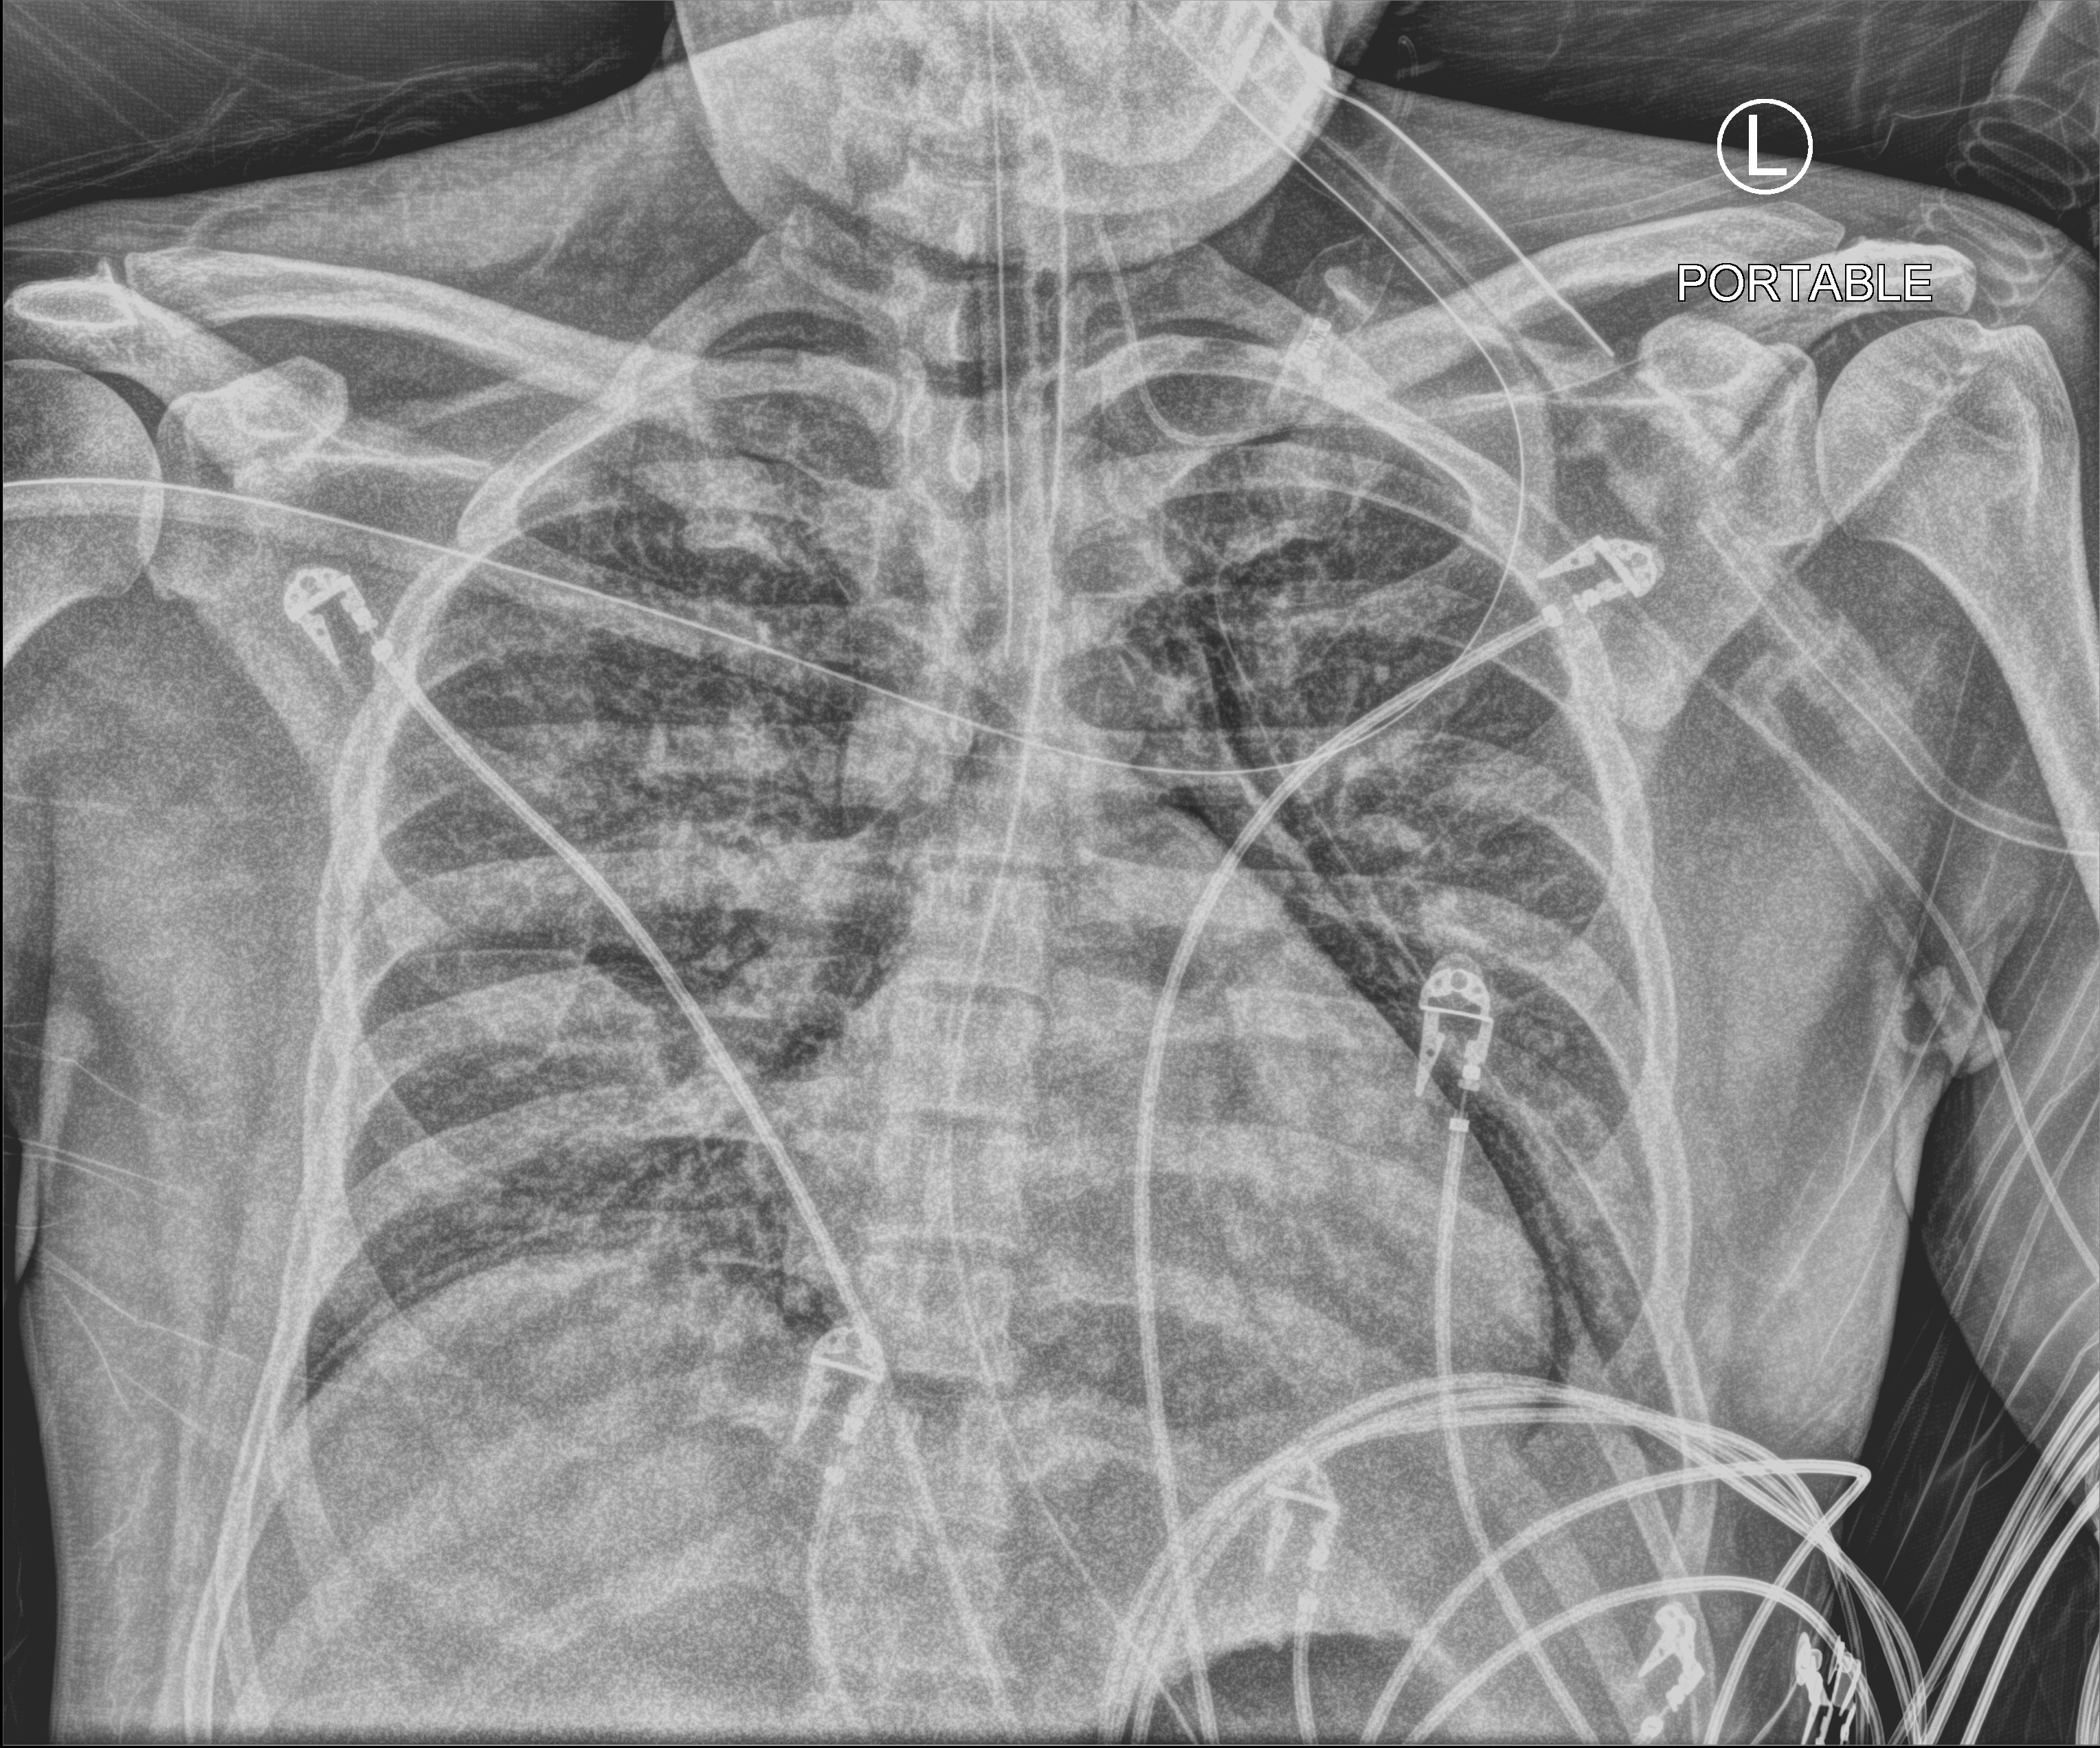
Bedside chest radiograph (computed radiography), anteroposterior (AP) projection. Male patient hospitalised with COVID-19, age 18–59 years.
Hospital-stay facts (about this admission, not read from this image; timing relative to this image not recorded):
- length of hospital stay: 30 days
- admitted to intensive care during this hospital stay: yes
- mechanically ventilated during this hospital stay: yes